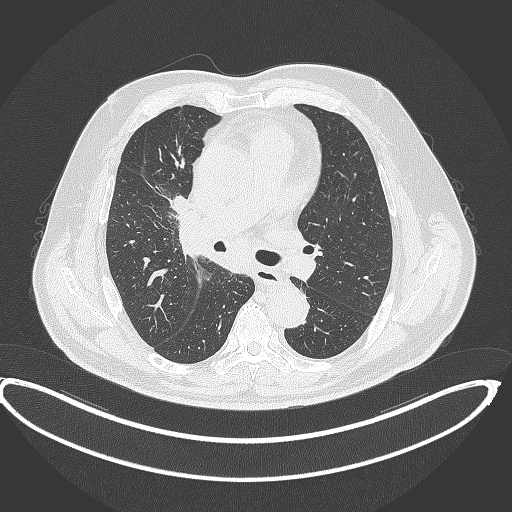
Chest CT, one axial slice; slice 243 of 390 in the series (ordered by position); reconstruction kernel B70f; lung window (W 1500 / L -600 HU); 512 × 512 image matrix. Male patient, age 62 years. From the clinical record (not read from this slice): clinical TNM (as recorded): T1c N3 M1c.
Annotated regions visible in this slice (bounding box drawn by a radiologist):
- lung tumour (recorded histology: adenocarcinoma): box from (x=167, y=195) to (x=191, y=214) px